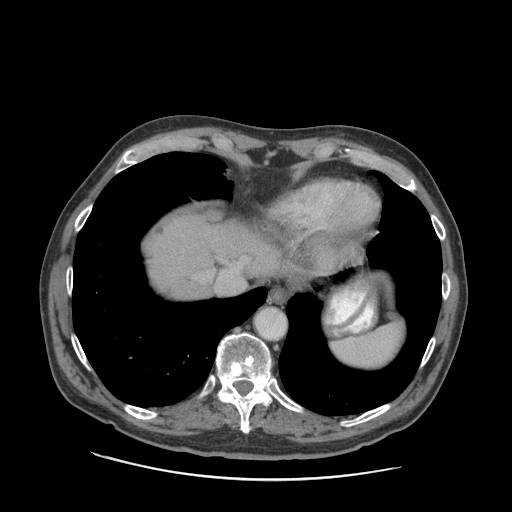
Contrast-enhanced abdominal CT (liver protocol), one axial slice; position 78 of 89 along the scan axis; 140 kVp; soft-tissue window (W 400 / L 40 HU); 512 × 512 image matrix, field of view 420 × 420 mm. From the clinical record (not read from this slice): diagnosis: hepatocellular carcinoma (patient treated with transarterial chemoembolisation; whether this scan precedes or follows treatment is not stated here); TNM stage (as recorded): Stage-I; Child-Pugh class: A; tumour nodularity: uninodular.
Outlined on this slice (semi-automatic segmentation, software-assisted and operator-edited):
- liver parenchyma outside the tumour (the mass and vessels are separate outlines, so this box may not span the whole liver): box from (x=144, y=214) to (x=332, y=300) px